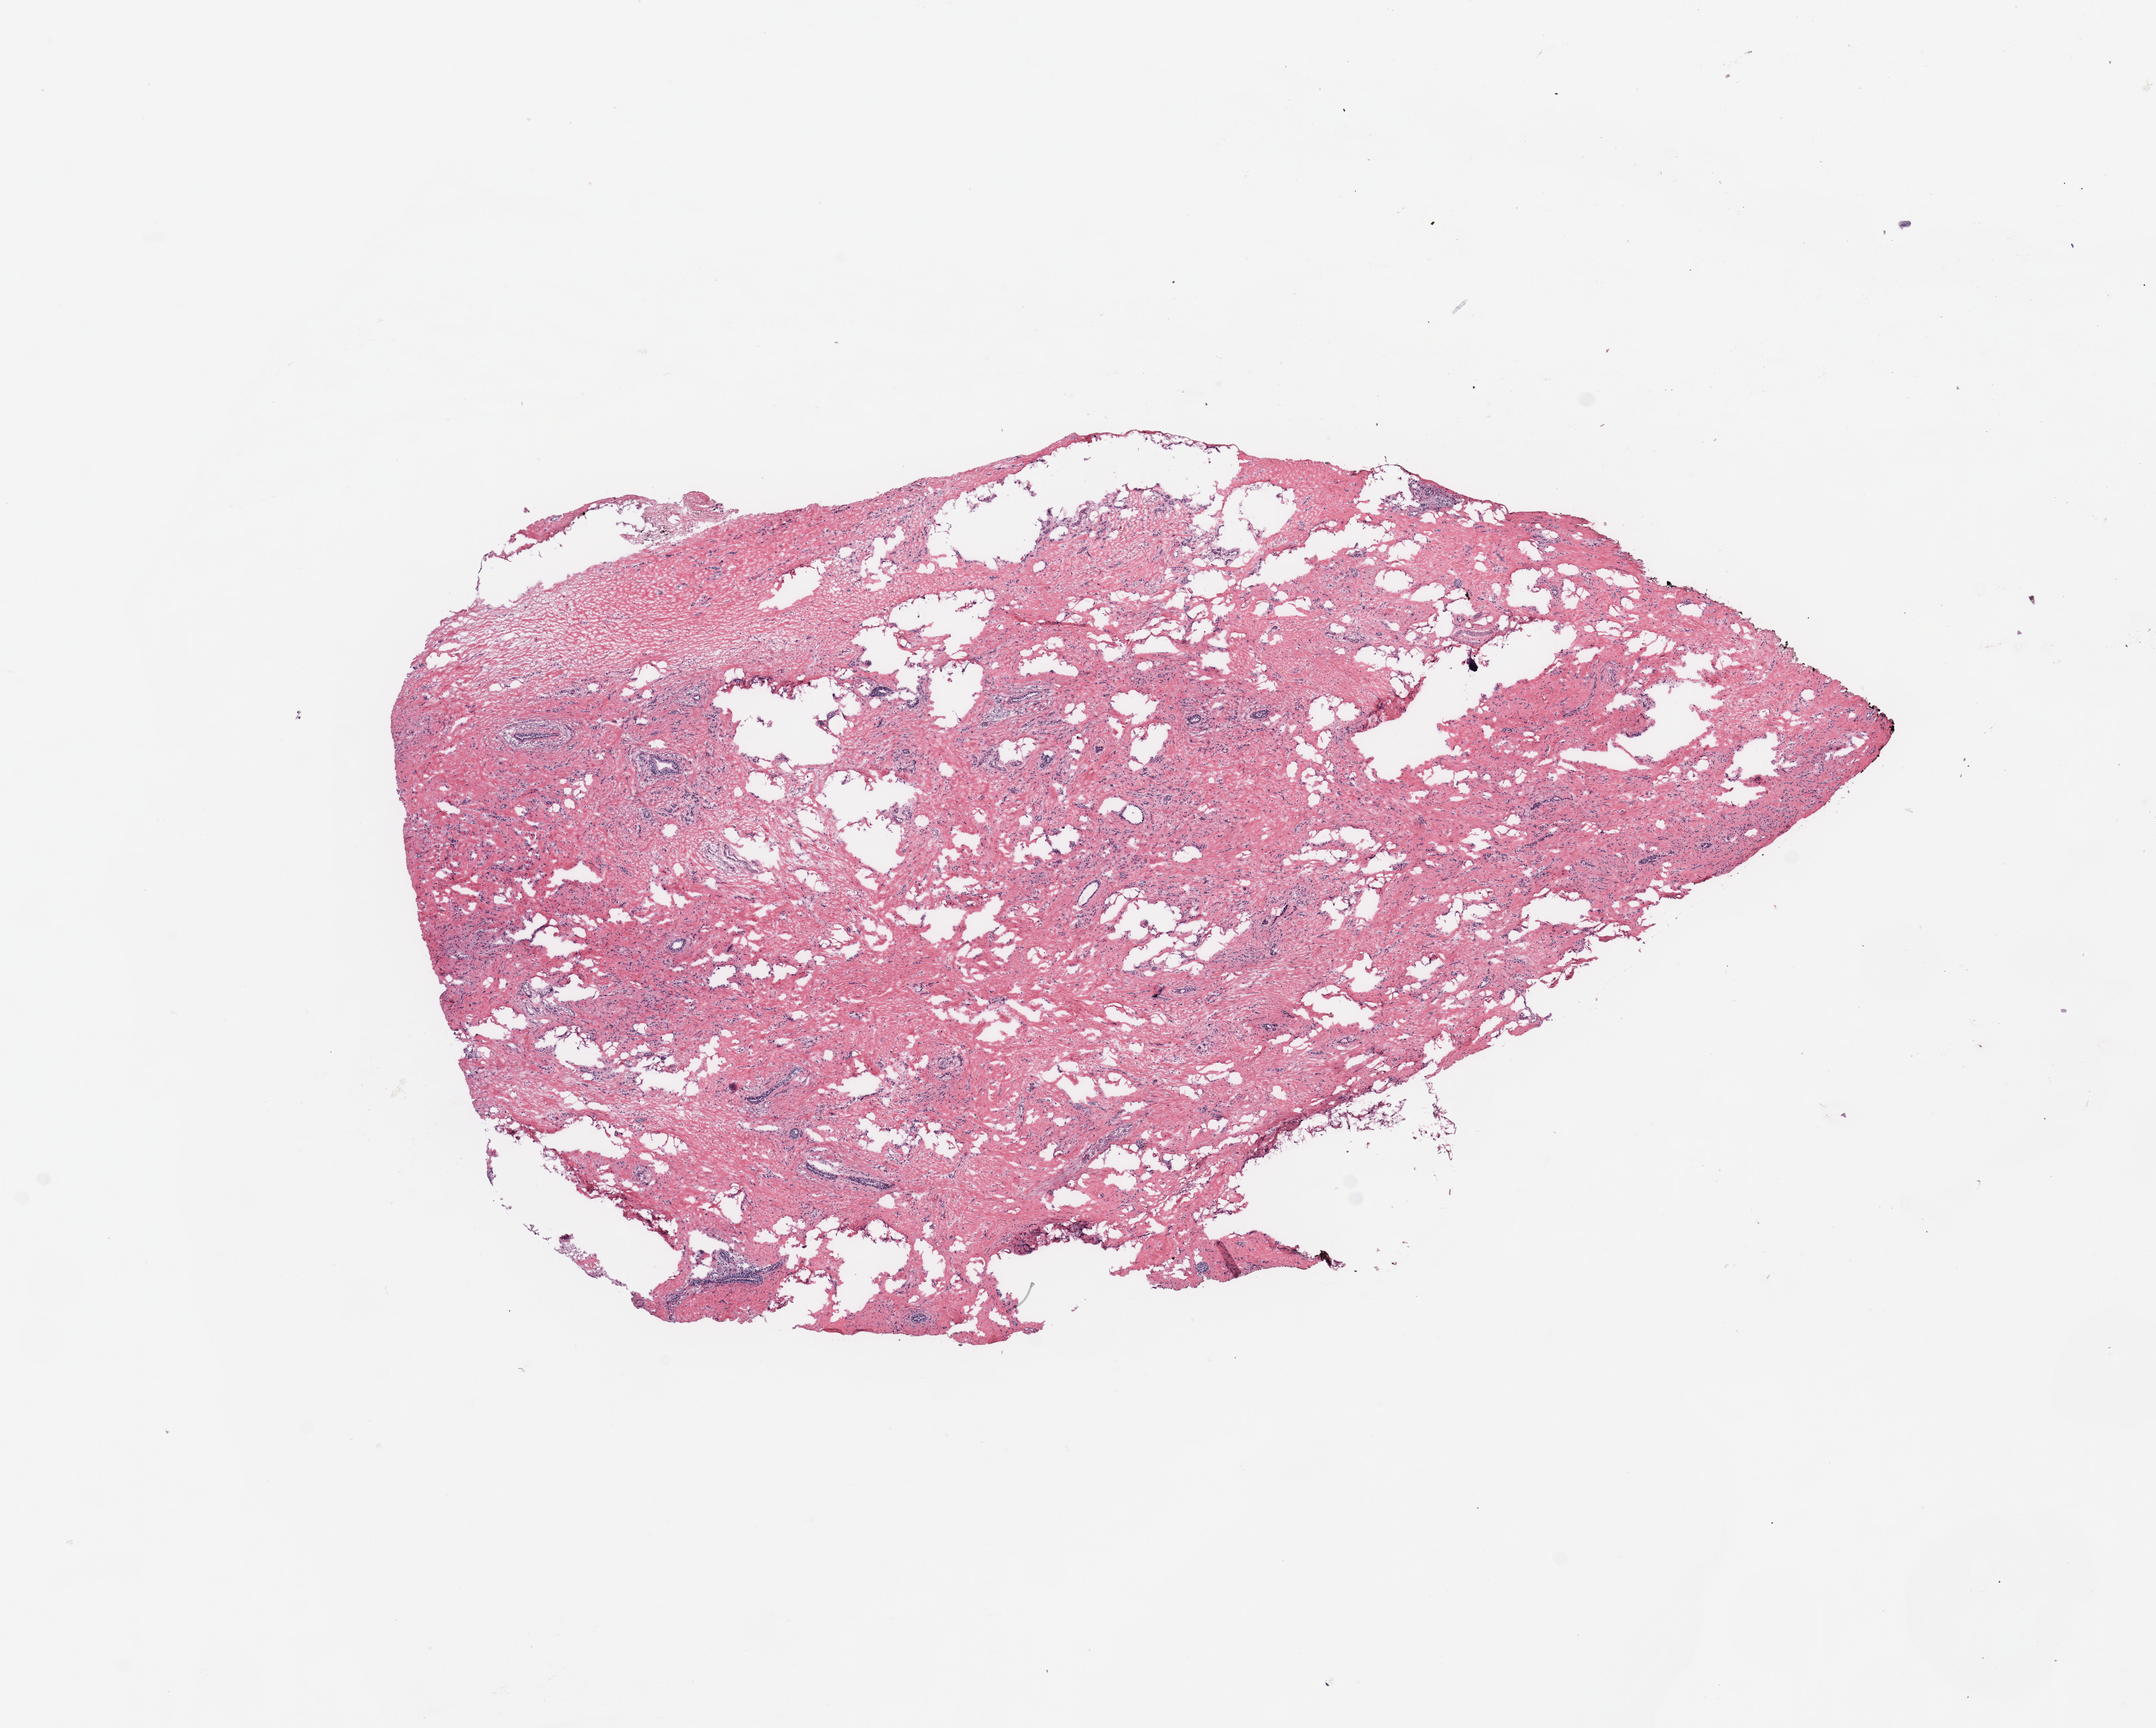
Whole-slide histology image, H&E-stained, whole scanned area (about 12.8 x 10.3 mm, acquisition: 20x scan) shown as a low-resolution overview, breast, tissue type not recorded.
Patient diagnosis (cohort enrolment): breast cancer (breast).